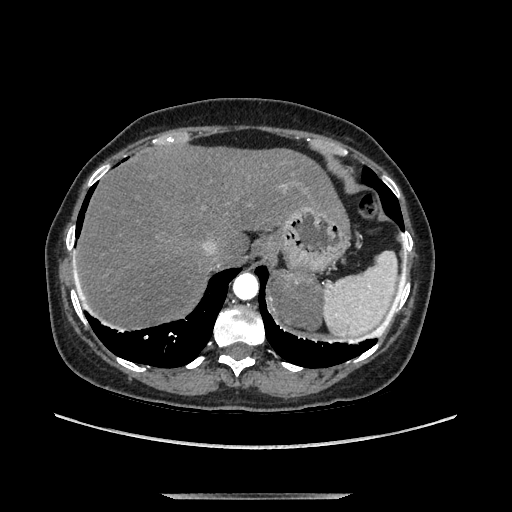
Contrast-enhanced abdominal CT, one axial slice; slice 113 of 169 in the series (ordered by position); soft-tissue window (W 400 / L 40 HU); 512 × 512 image matrix, field of view 400 × 400 mm. Female patient. From the clinical record (not read from this slice): diagnosis: adrenocortical carcinoma; tumour side: left adrenal; tumour size at pathology: 9 cm; Ki-67 index: 2 %; stage (as recorded): 3.
Outlined on this slice (semi-automatic segmentation, software-assisted and operator-edited):
- mass: bounding box (x1, y1, x2, y2) in pixels: (274, 276, 320, 329)